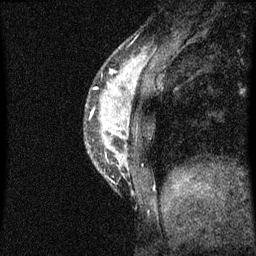
Breast MRI (dynamic contrast-enhanced), one sagittal slice; position 17 of 60 along the scan axis; dynamic contrast-enhanced series, image 2 of 3 at this slice position (ordered by acquisition); 1.5 T; TE 4.2 ms, TR 8 ms; 2 mm slice thickness; 256 × 256 image matrix, field of view 180 × 180 mm. Patient: female, 33 years.
Structures marked on this image (semi-automatic segmentation, software-assisted and operator-edited):
- analysis volume of interest (the breast-tissue region the enhancement analysis was run in; not a lesion): bounding box [x1, y1, x2, y2] px = [85, 58, 151, 191]
- tumour enhancement mask (voxels above the 70 % enhancement threshold inside the analysis volume of interest): [95, 66, 131, 117]